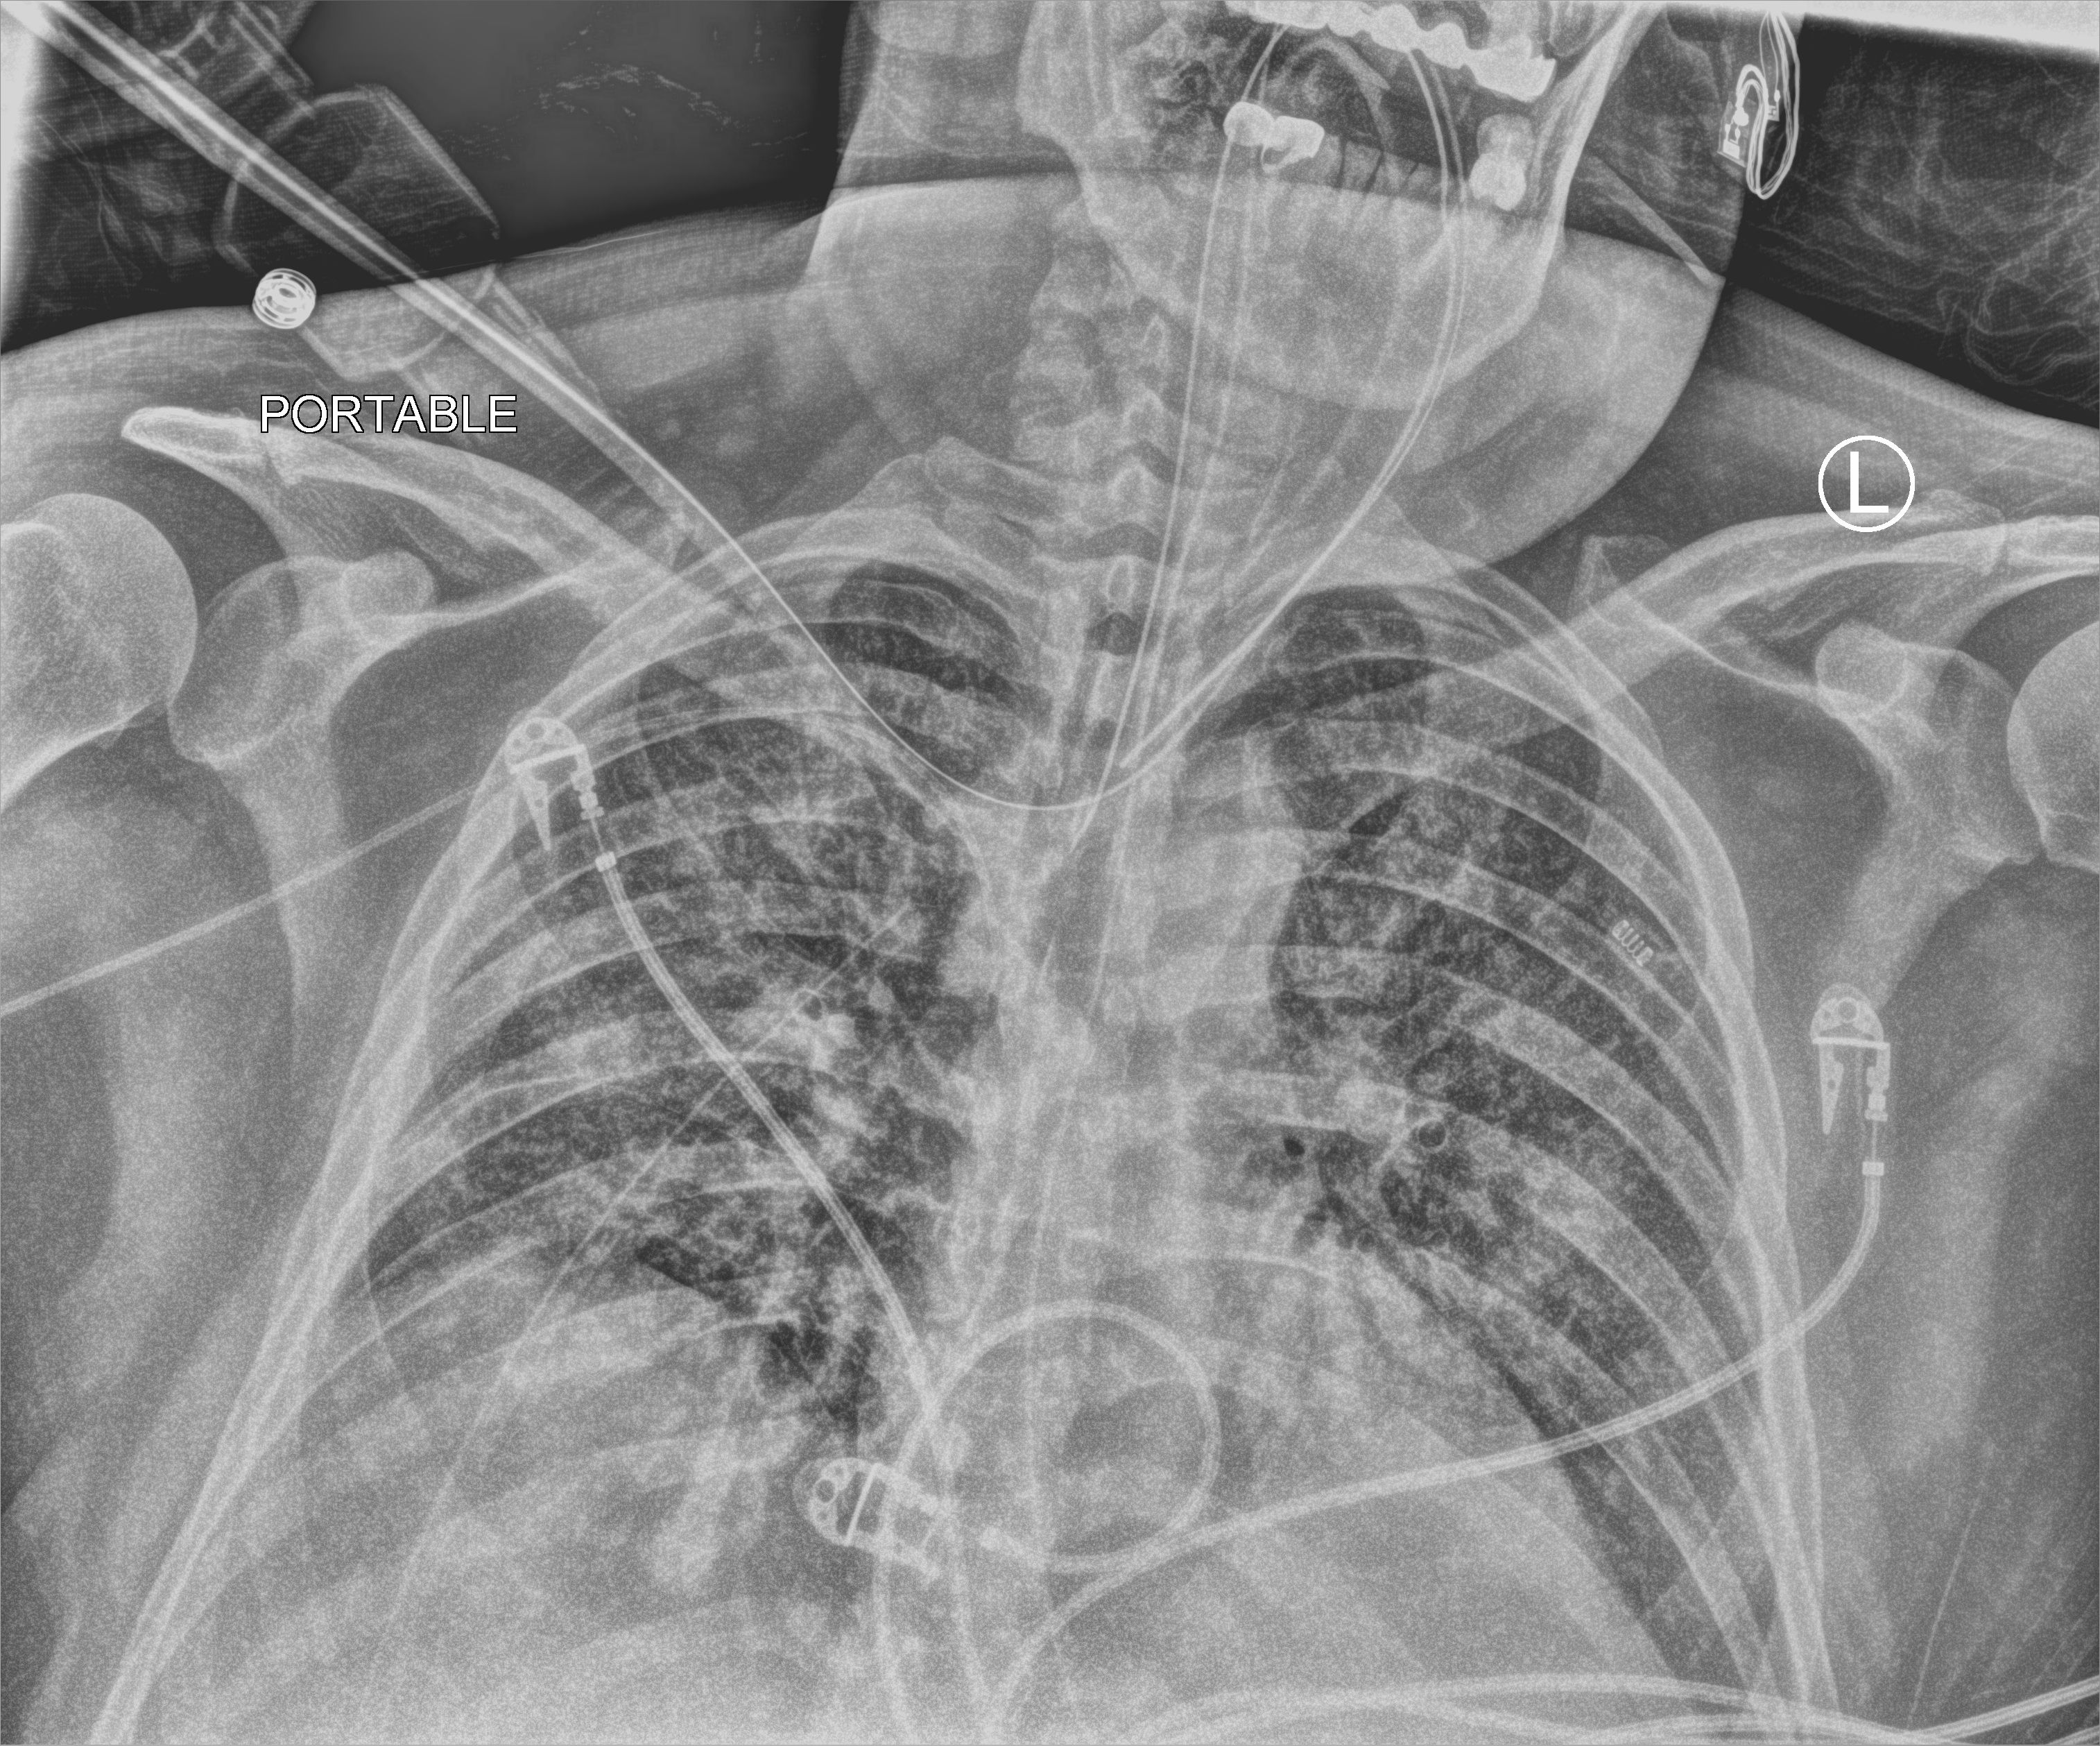
Bedside chest radiograph (computed radiography). Male patient hospitalised with COVID-19, age 18–59 years.
Admission-level facts for this patient (not findings on this image; timing relative to this image not recorded):
- length of hospital stay: 96 days